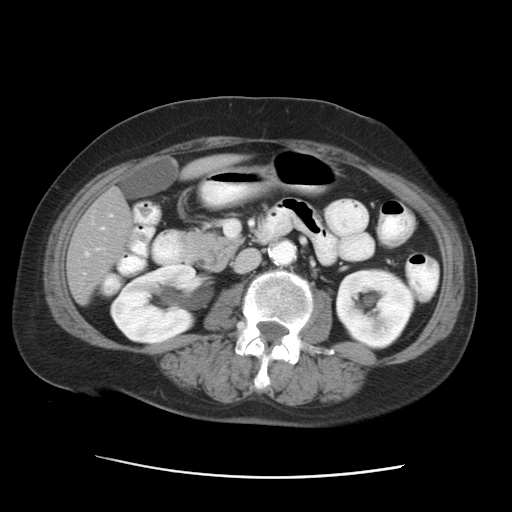
Contrast-enhanced abdominal CT, one axial slice; slice 10 of 29 in the series (ordered by position); reconstruction kernel STANDARD; 120 kVp; intravenous contrast given; soft-tissue window (W 400 / L 40 HU); 512 × 512 image matrix, field of view 354 × 354 mm. Female patient, age 64 years. Case-level facts recorded for this patient, not image findings: diagnosis: colorectal cancer liver metastases, imaged before liver resection; multiple liver metastases: no; largest metastasis: 2.5 cm.
Annotated regions visible in this slice (outlined manually by an expert reader):
- liver: bounding box <67,155,240,303> (left, top, right, bottom; pixels)
- planned liver remnant (the part of the liver to remain after resection): <67,155,241,303>
- portal vein (with intrahepatic branches): <224,219,237,238>